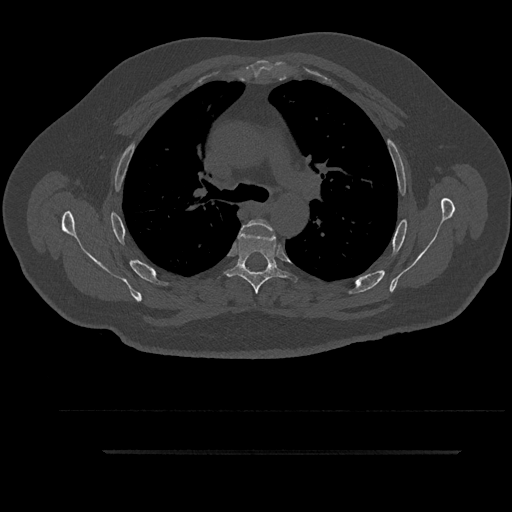
CT including the spine, one axial slice. Slice 633 of 797 in the series (ordered by position). 120 kVp. Bone window (W 1800 / L 400 HU). 0.5 mm slice thickness. 512 × 512 image matrix, field of view 432 × 432 mm. Patient: male, 63 years. Case-level facts recorded for this patient, not image findings: primary cancer: renal; vertebrae with lytic lesions (as recorded): T8.
Annotated regions visible in this slice (semi-automatically segmented with operator editing):
- T4 vertebra: box from (x=241, y=219) to (x=272, y=231) px
- T5 vertebra: (x=226, y=226)–(x=298, y=294)
- T6 vertebra: (x=263, y=269)–(x=266, y=272)